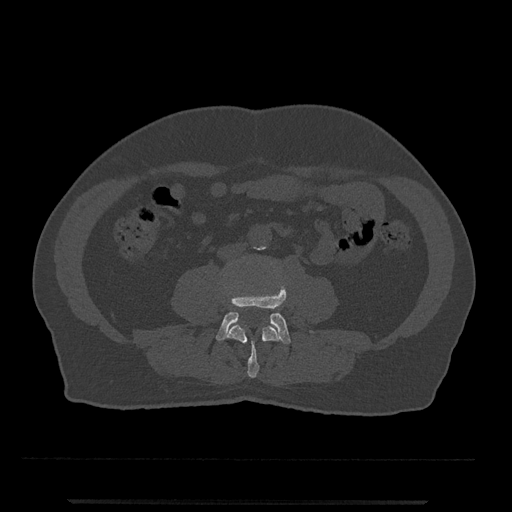
CT including the spine, one axial slice. Slice 167 of 797 in the series (ordered by position). Reconstruction kernel Br40s/3. Bone window (W 1800 / L 400 HU). 0.5 mm slice thickness. 512 × 512 image matrix. Patient: male, 63 years. From the clinical record (not read from this slice): primary cancer: prostate.
Outlined on this slice (semi-automatic segmentation, software-assisted and operator-edited):
- L3 vertebra: box from (x=227, y=324) to (x=281, y=378) px
- L4 vertebra: (x=216, y=288)–(x=291, y=345)